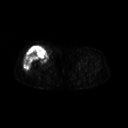
FDG PET of an extremity soft-tissue mass (from a PET/CT study), one axial slice. Position 239 of 311 along the scan axis. 3.27 mm slice thickness. 128 × 128 image matrix. Patient: female, 57 years. From the clinical record (not read from this slice): histological type: pleiomorphic undifferentiated sarcoma; grade: high; site of the primary tumour: right quadricep.
Structures marked on this image (expert contour drawn on MRI and transferred to this co-registered scan by the dataset authors):
- tumour plus oedema (research contour): box from (x=24, y=48) to (x=47, y=70) px
- tumour (research contour): (x=24, y=48)–(x=47, y=70)